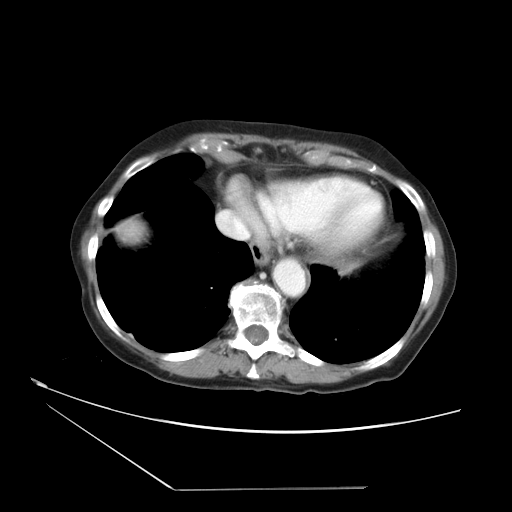
Contrast-enhanced abdominal CT, one axial slice. Slice 33 of 36 in the series (ordered by position). Soft-tissue window (W 400 / L 40 HU). 5 mm slice thickness. 512 × 512 image matrix, field of view 384 × 384 mm. Female patient, age 81 years. From the clinical record (not read from this slice): diagnosis: colorectal cancer liver metastases, imaged before liver resection; multiple liver metastases: no; largest metastasis: 1.6 cm; disease in both lobes: no.
Outlined on this slice (outlined manually by an expert reader):
- liver: box from (x=116, y=218) to (x=148, y=246) px
- planned liver remnant (the part of the liver to remain after resection): (x=116, y=218)–(x=148, y=246)